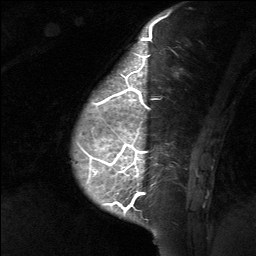
Breast MRI (dynamic contrast-enhanced), one sagittal slice. Slice 16 of 64 in the series (ordered by position). Dynamic contrast-enhanced study with each time point stored as its own series, time point 2 of 3 at this slice position (early post-contrast, ordered by acquisition time). 1.5 T. TE 4.8 ms, TR 27 ms. 2 mm slice thickness. 256 × 256 image matrix, field of view 180 × 180 mm. Patient: female, 39 years. Case-level facts recorded for this patient, not image findings: setting: breast cancer imaged before/during neoadjuvant chemotherapy; receptor status: HER2-positive.
Annotated regions visible in this slice (semi-automatic segmentation, software-assisted and operator-edited):
- analysis volume of interest (the breast-tissue region the enhancement analysis was run in; not a lesion): bounding box [x1, y1, x2, y2] px = [70, 40, 201, 217]
- tumour enhancement mask (voxels above the 90 % enhancement threshold inside the analysis volume of interest): [90, 40, 157, 213]